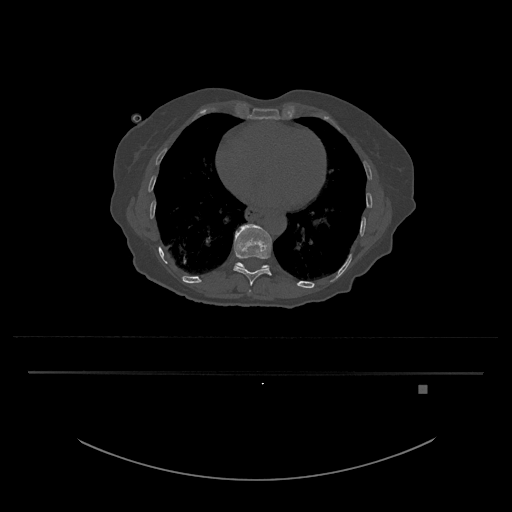
CT including the spine, one axial slice. Position 704 of 797 along the scan axis. 120 kVp. Bone window (W 1800 / L 400 HU). 0.5 mm slice thickness. 512 × 512 image matrix. Patient: female, 57 years. From the clinical record (not read from this slice): primary cancer: cervical.
Outlined on this slice (semi-automatically segmented with operator editing):
- T10 vertebra: bounding box [x1, y1, x2, y2] px = [233, 224, 272, 286]
- T11 vertebra: [236, 262, 270, 270]